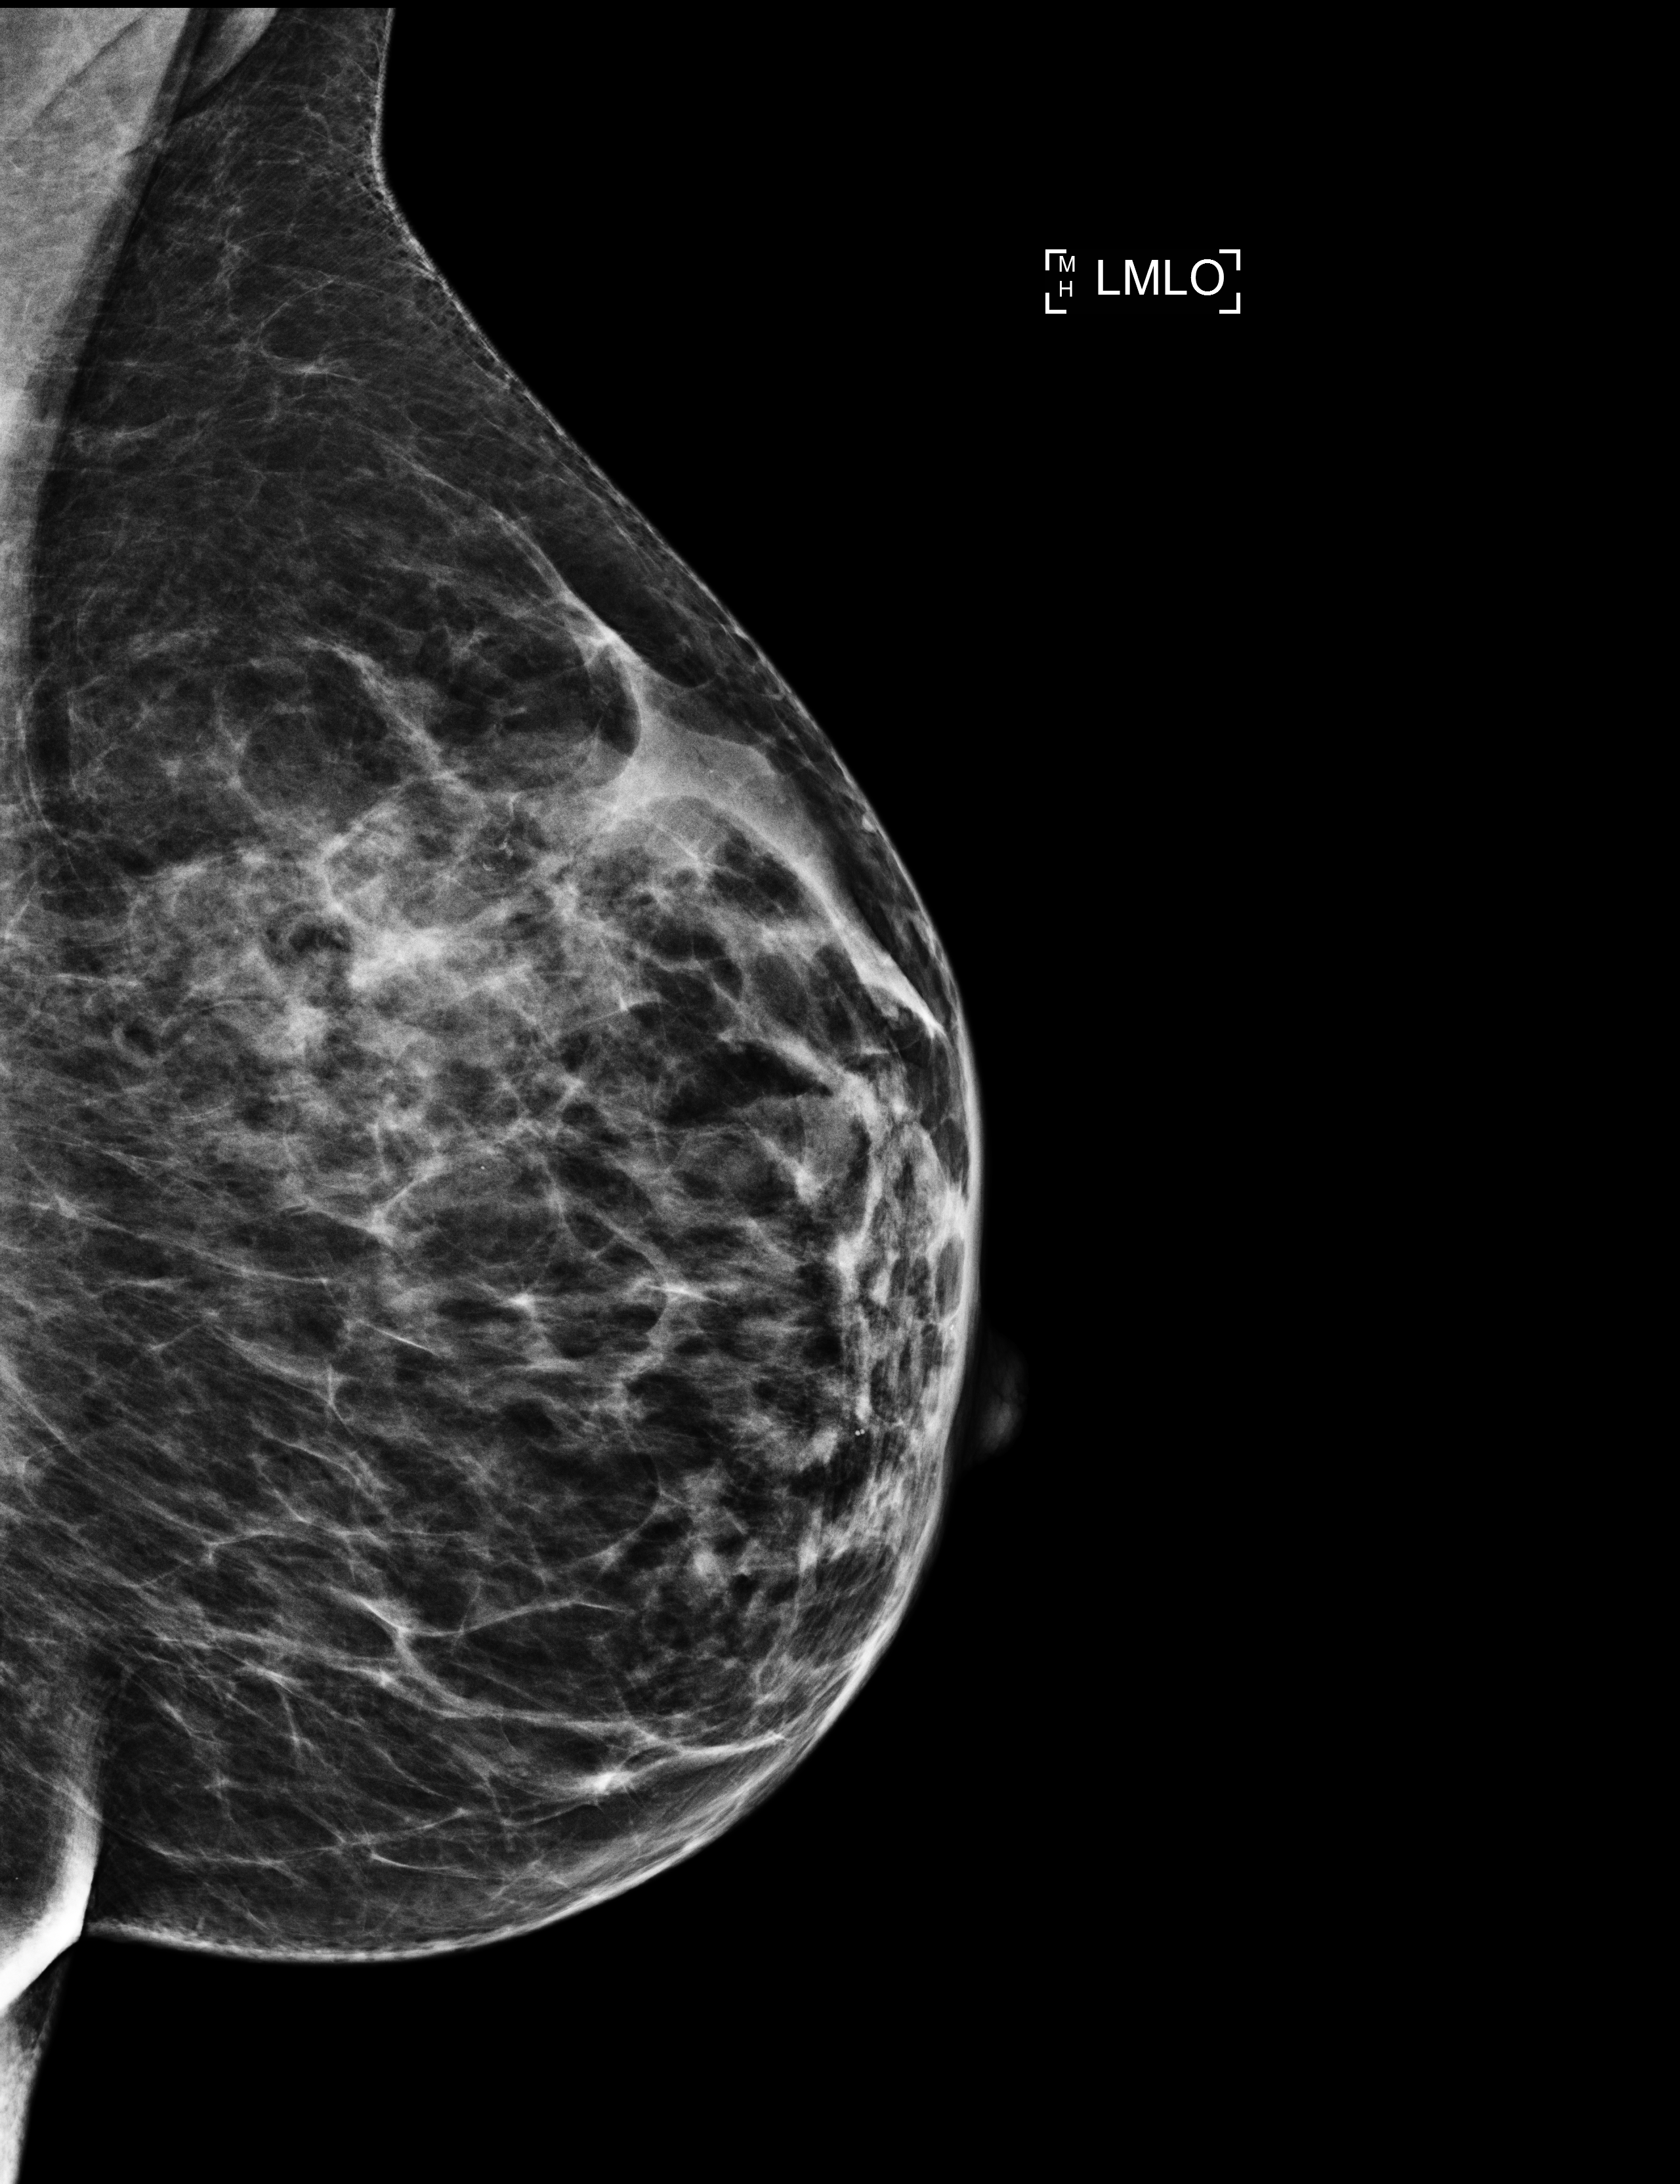
Annual screening mammography examination; compressed breast thickness 42 mm.
Image type: full-field digital mammogram. Breast: left. Projection: medio-lateral oblique projection.